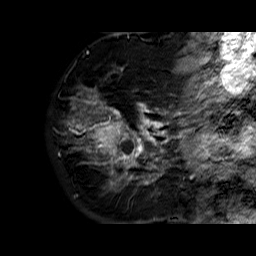
Breast MRI (dynamic contrast-enhanced), one sagittal slice; dynamic contrast-enhanced series, time point 2 of 6 at this slice position (early post-contrast); 1.5 T; TE 6.3 ms, TR 32.4 ms; 4 mm slice thickness; 256 × 256 image matrix. Female patient. From the clinical record (not read from this slice): setting: breast cancer imaged before/during neoadjuvant chemotherapy; receptor status: HR-positive, HER2-negative.
Structures marked on this image (semi-automatic segmentation, software-assisted and operator-edited):
- analysis volume of interest (the breast-tissue region the enhancement analysis was run in; not a lesion): bounding box <70,72,177,183> (left, top, right, bottom; pixels)
- tumour enhancement mask (voxels above the 100 % enhancement threshold inside the analysis volume of interest): <82,89,177,183>